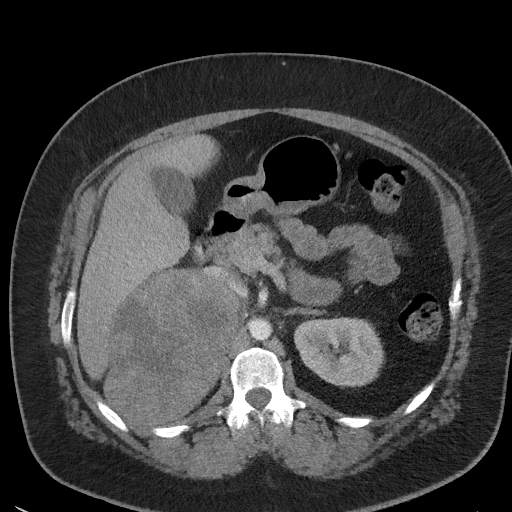
Contrast-enhanced abdominal CT, one axial slice; position 29 of 56 along the scan axis; reconstruction kernel I41f/3; 120 kVp; intravenous contrast given; soft-tissue window (W 400 / L 40 HU); 512 × 512 image matrix. Patient: female, 35 years. Case-level facts recorded for this patient, not image findings: diagnosis: adrenocortical carcinoma; tumour side: right adrenal; tumour size at pathology: 15 cm; Ki-67 index: 40 %; stage (as recorded): 2.
Outlined on this slice (semi-automatic segmentation, software-assisted and operator-edited):
- mass: bounding box (x1, y1, x2, y2) in pixels: (107, 272, 234, 419)